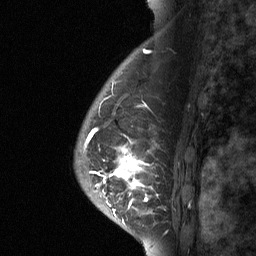
Breast MRI (dynamic contrast-enhanced), one sagittal slice. Dynamic contrast-enhanced study with each time point stored as its own series, time point 2 of 3 at this slice position (early post-contrast, ordered by acquisition time). 1.5 T. TE 4.8 ms, TR 27 ms. 256 × 256 image matrix. Female patient, age 56 years. From the clinical record (not read from this slice): setting: breast cancer imaged before/during neoadjuvant chemotherapy; receptor status: HER2-positive.
Outlined on this slice (semi-automatic segmentation, software-assisted and operator-edited):
- analysis volume of interest (the breast-tissue region the enhancement analysis was run in; not a lesion): box from (x=97, y=104) to (x=182, y=229) px
- tumour enhancement mask (voxels above the 90 % enhancement threshold inside the analysis volume of interest): (x=98, y=105)–(x=151, y=212)